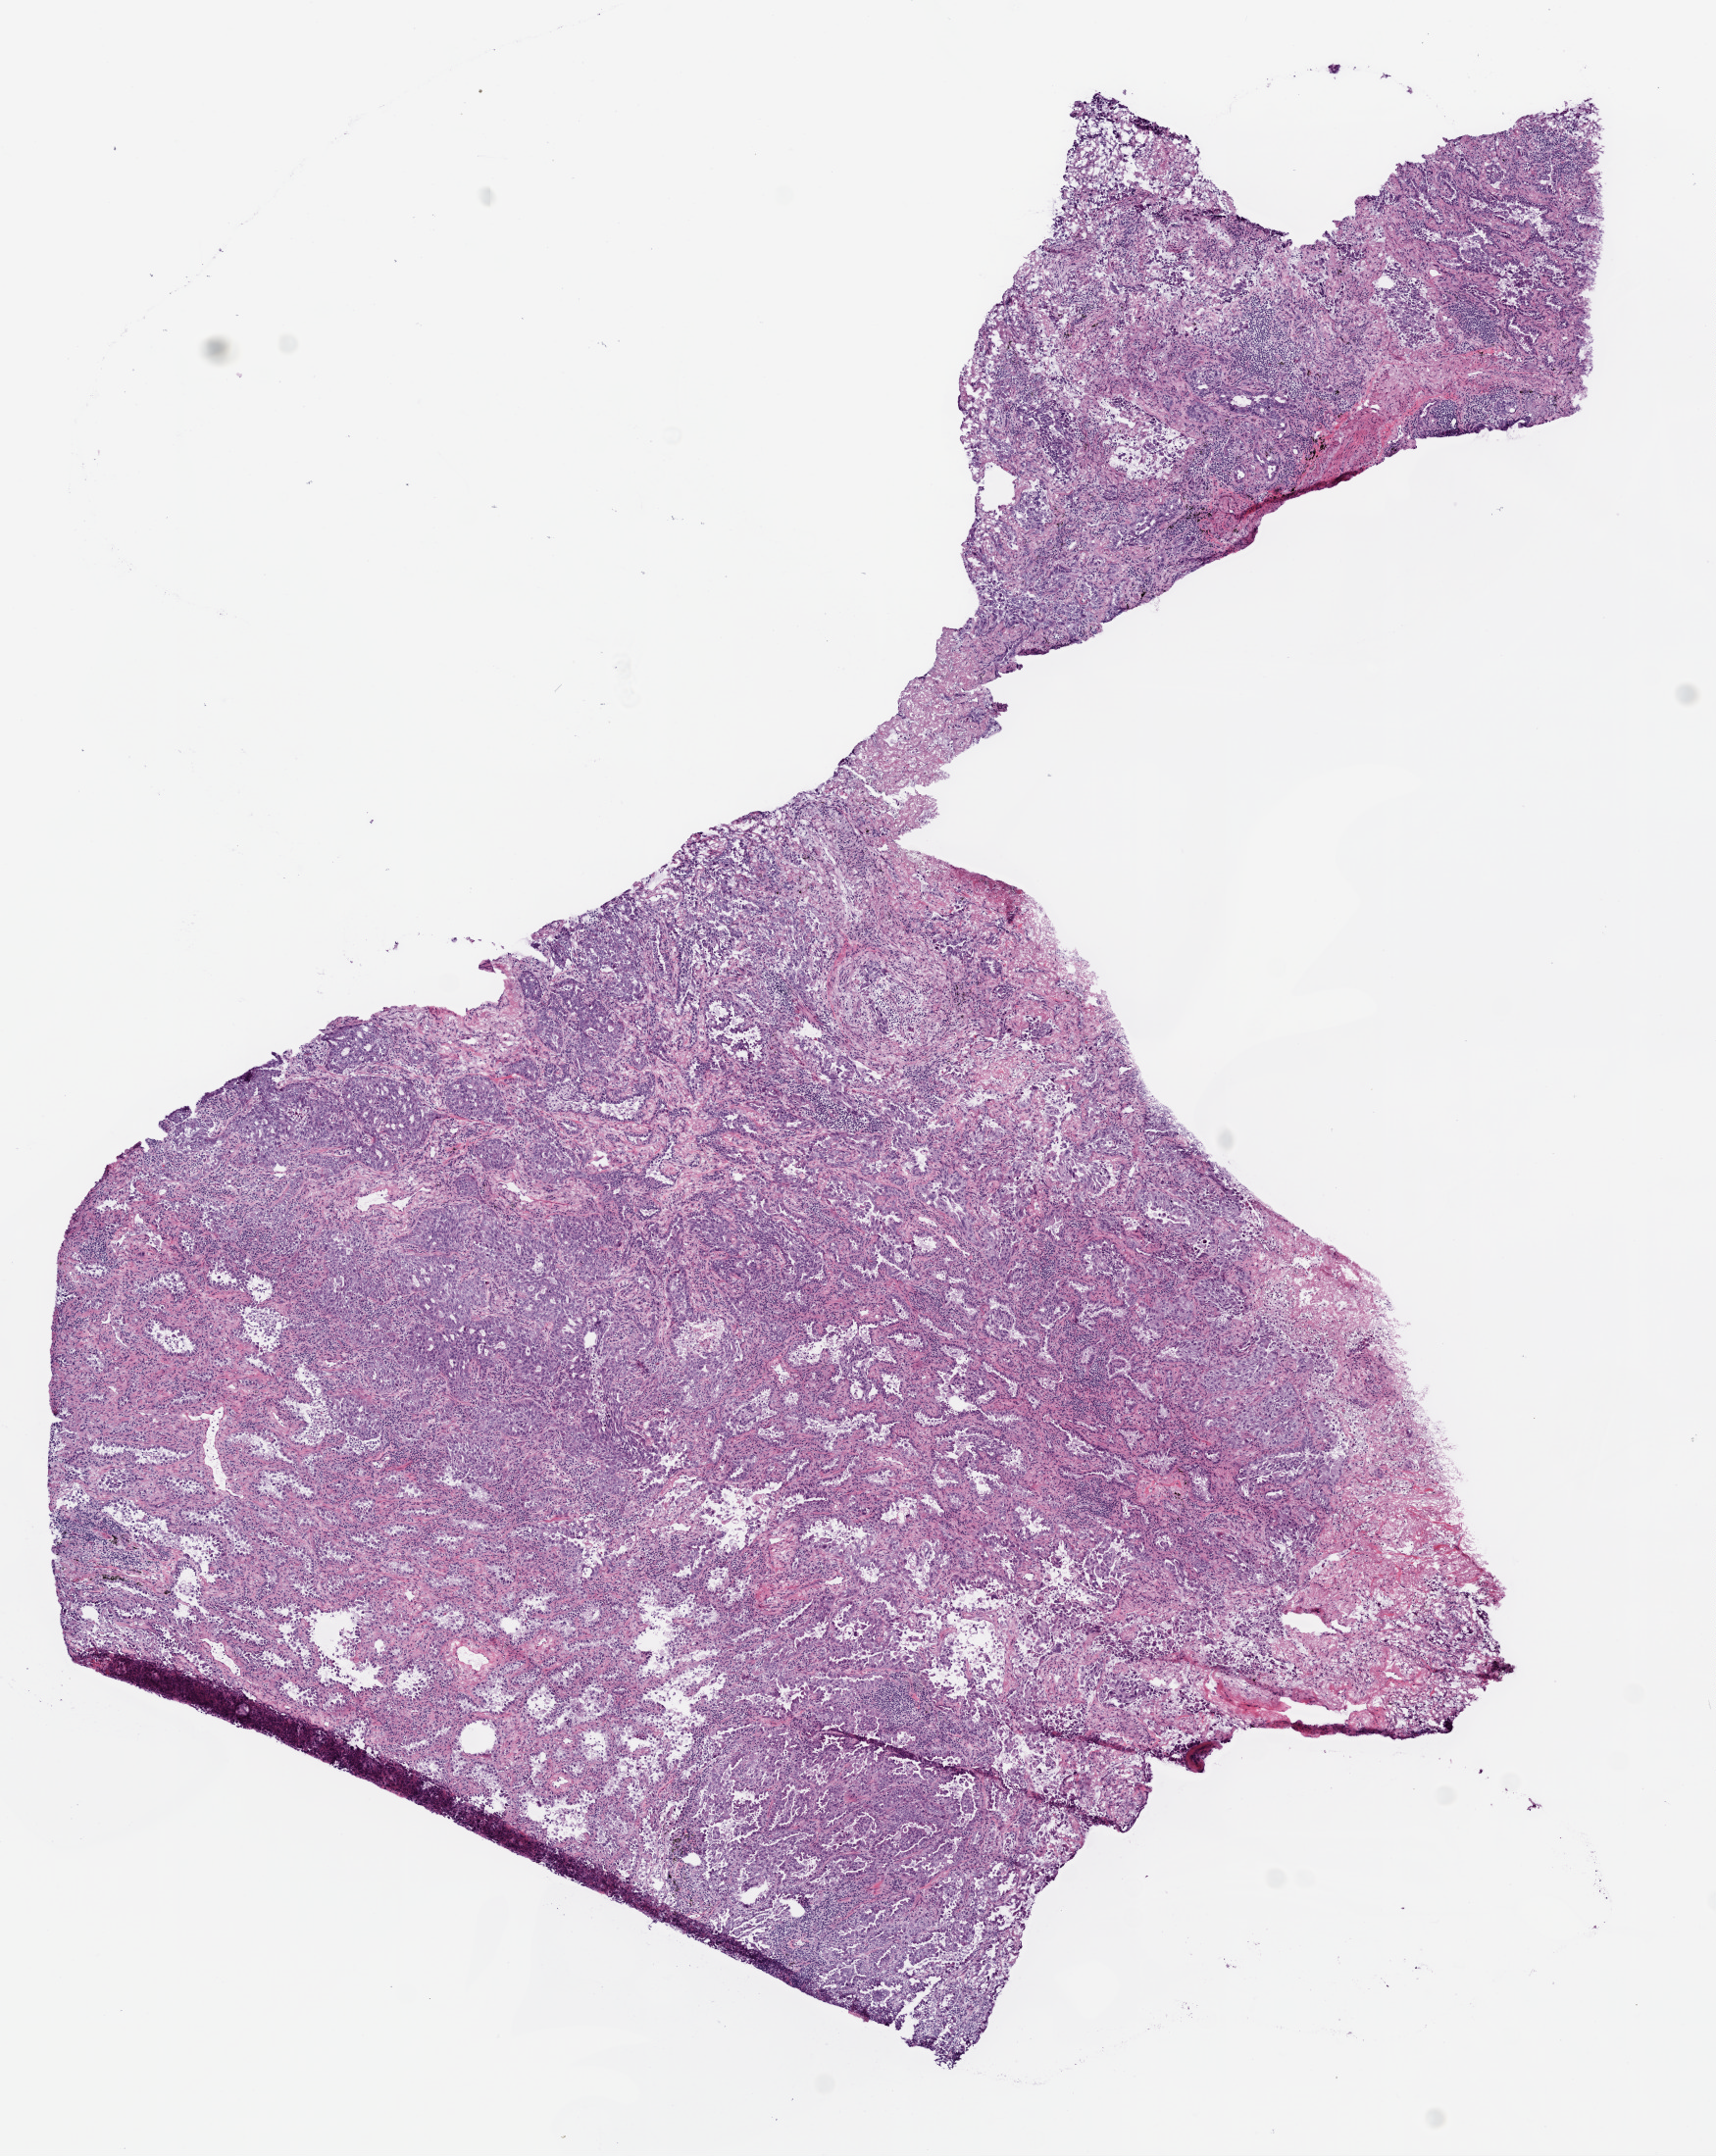
H&E whole-slide image, low-resolution overview of the scanned area, about 7.0 x 8.8 mm. Frozen section. Sample: primary tumour, lung. Female patient; age at initial diagnosis 71 years. Composition of this section per pathologist review: tumour cells 100%, tumour nuclei 80%, necrosis 0%. Inflammatory infiltration, as recorded: lymphocyte infiltration 15%.
• diagnosis: Adenocarcinoma, NOS (upper lobe, lung)
• AJCC pathologic stage: IA (7th edition)